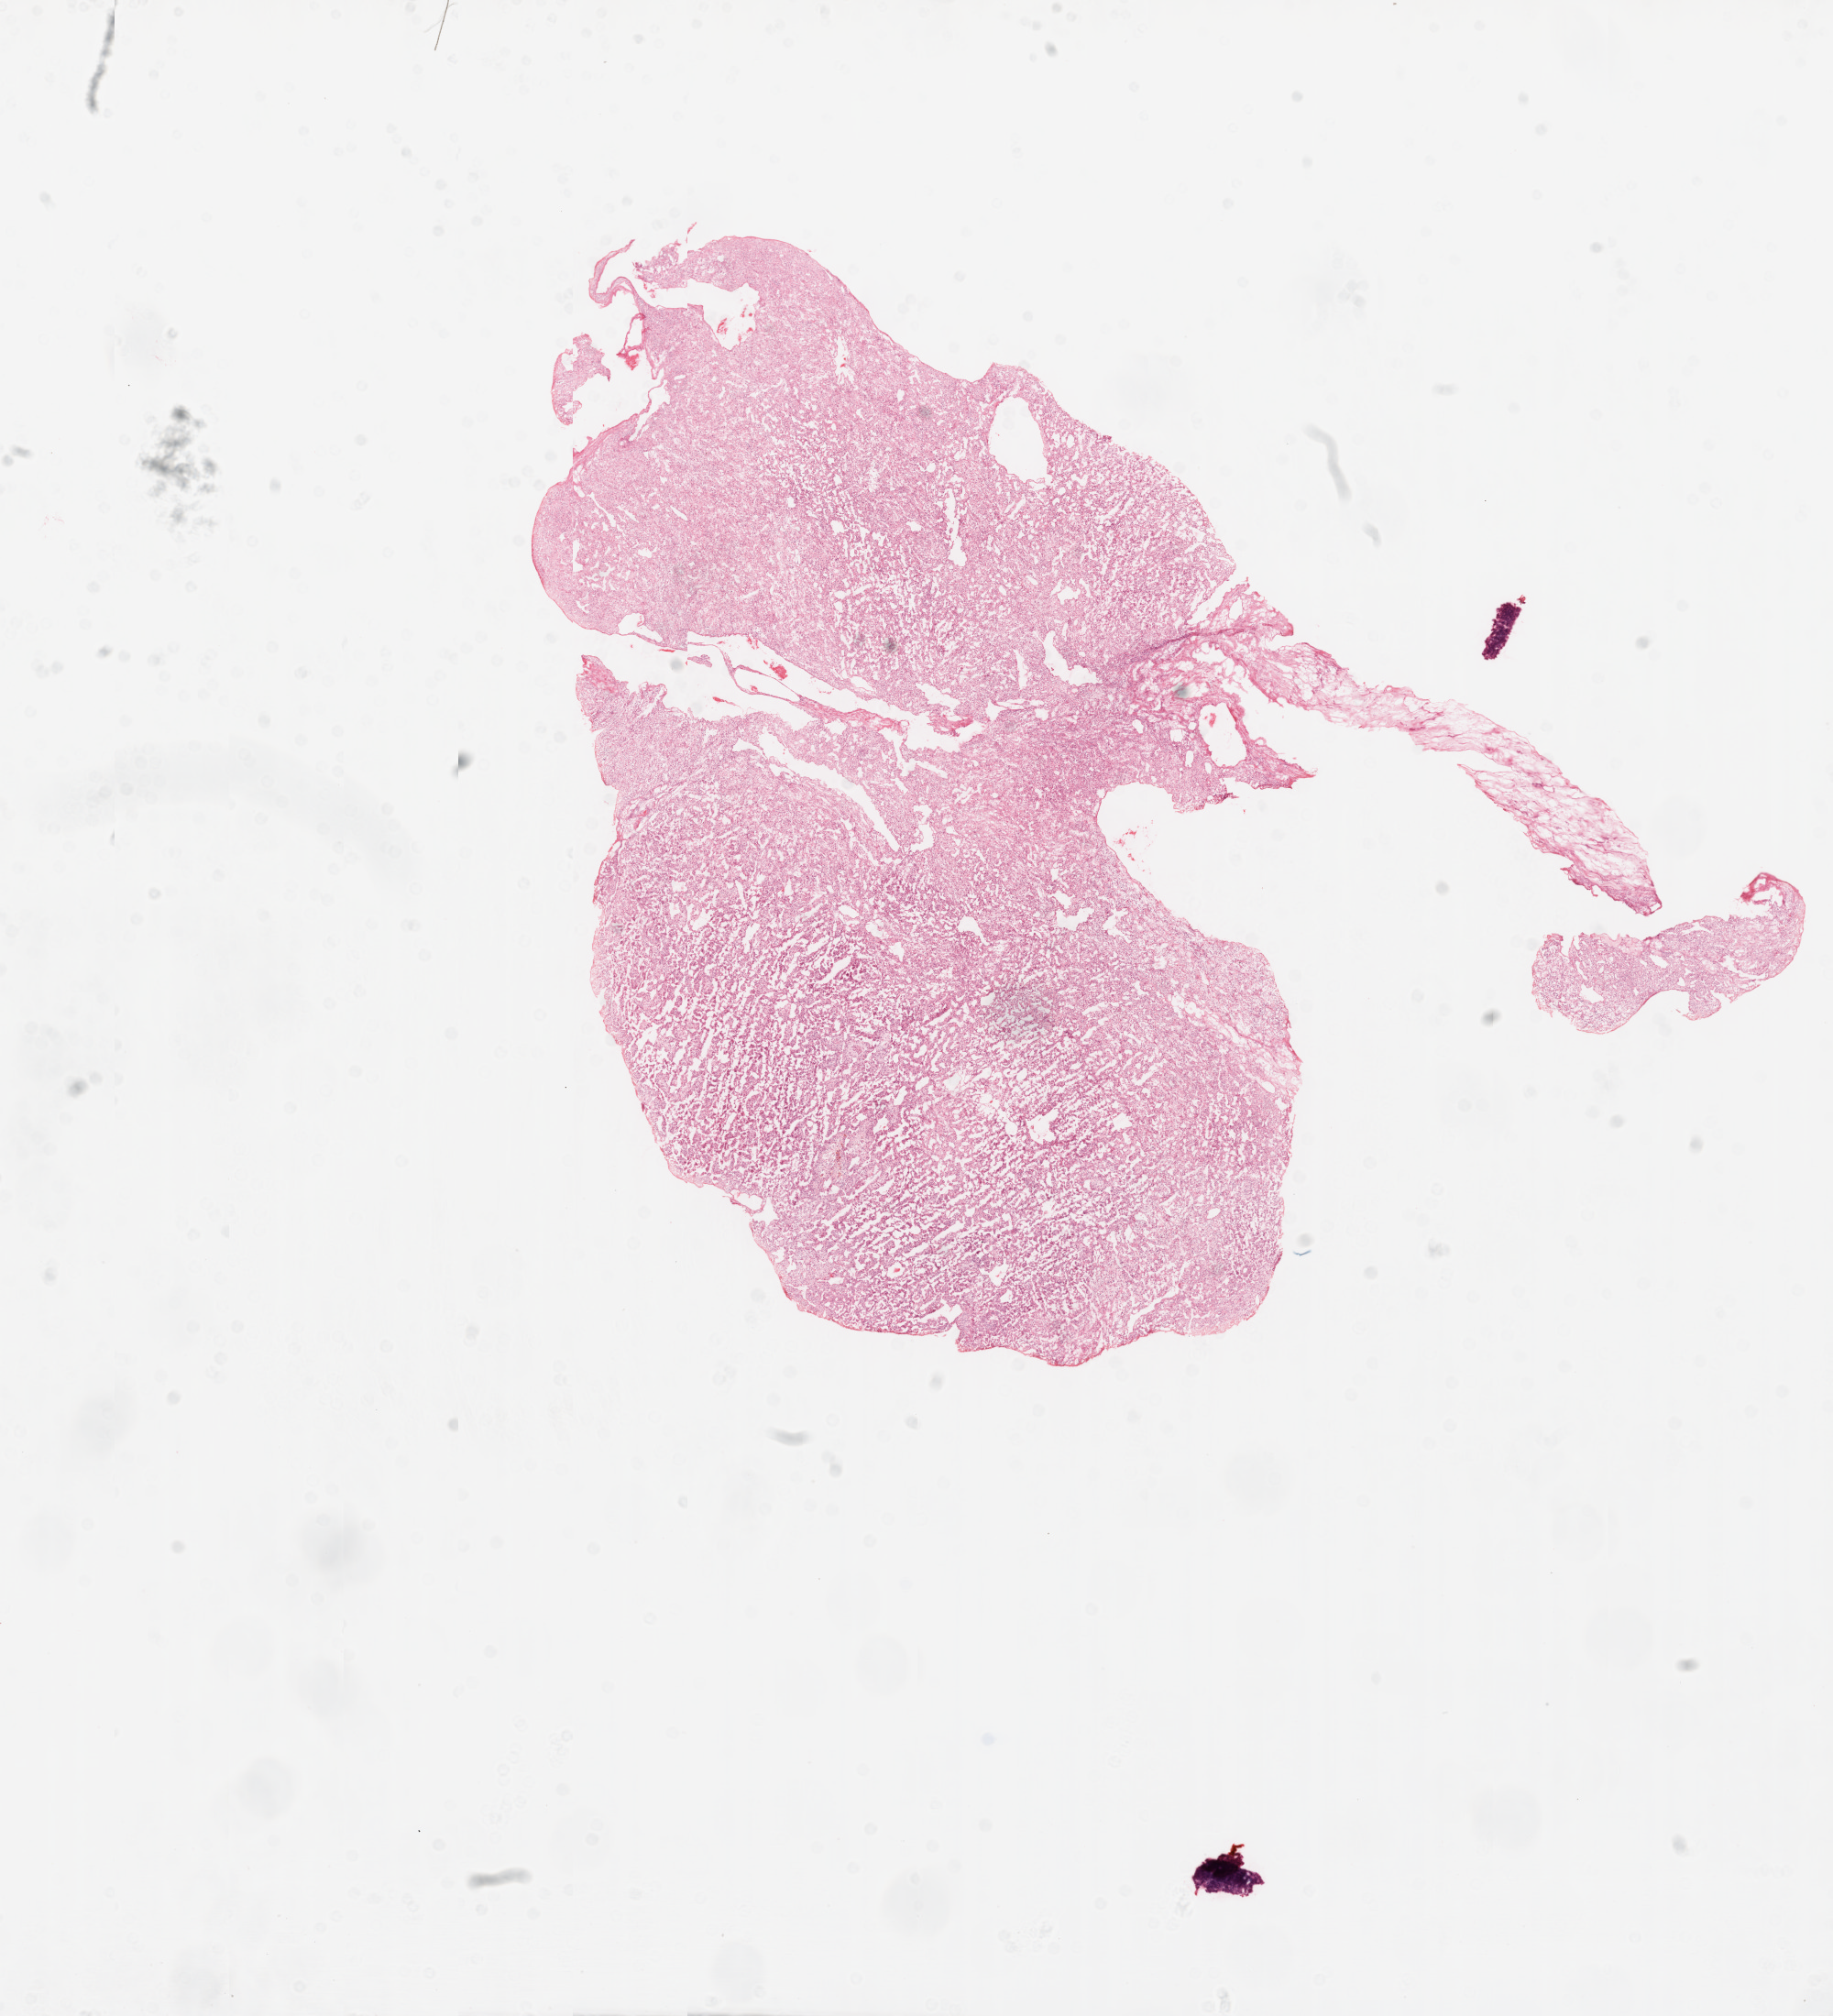
H&E-stained whole-slide image, whole scanned area (about 16.0 x 17.7 mm, acquisition: 20x scan) shown as a low-resolution overview, frozen section, kidney, primary tumour sample. Patient sex: male. Histologic grade: G3 (poorly differentiated). Composition of this section per pathologist review: tumour cells 95%, tumour nuclei 90%, normal cells 0%, stromal cells 5%, necrosis 0%.
AJCC pathologic stage: II. Laterality: left. Diagnosis: Clear cell adenocarcinoma, NOS.